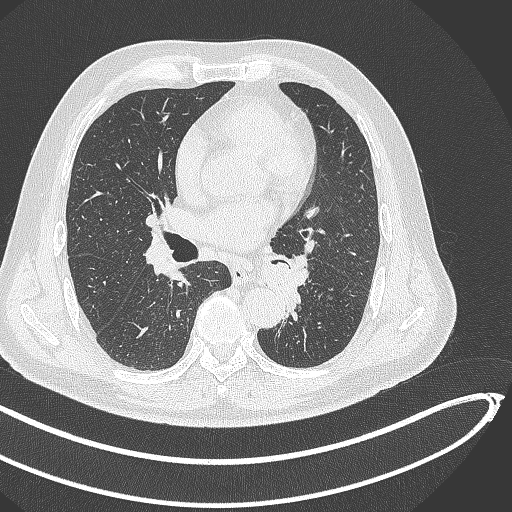
Chest CT, one axial slice; slice 246 of 468 in the series (ordered by position); 120 kVp; lung window (W 1500 / L -600 HU); 512 × 512 image matrix. Patient: male, 64 years. Case-level facts recorded for this patient, not image findings: clinical TNM (as recorded): T1c N0 M0.
Annotated regions visible in this slice (bounding box drawn by a radiologist):
- lung tumour (recorded histology: squamous cell carcinoma): box from (x=261, y=256) to (x=301, y=325) px